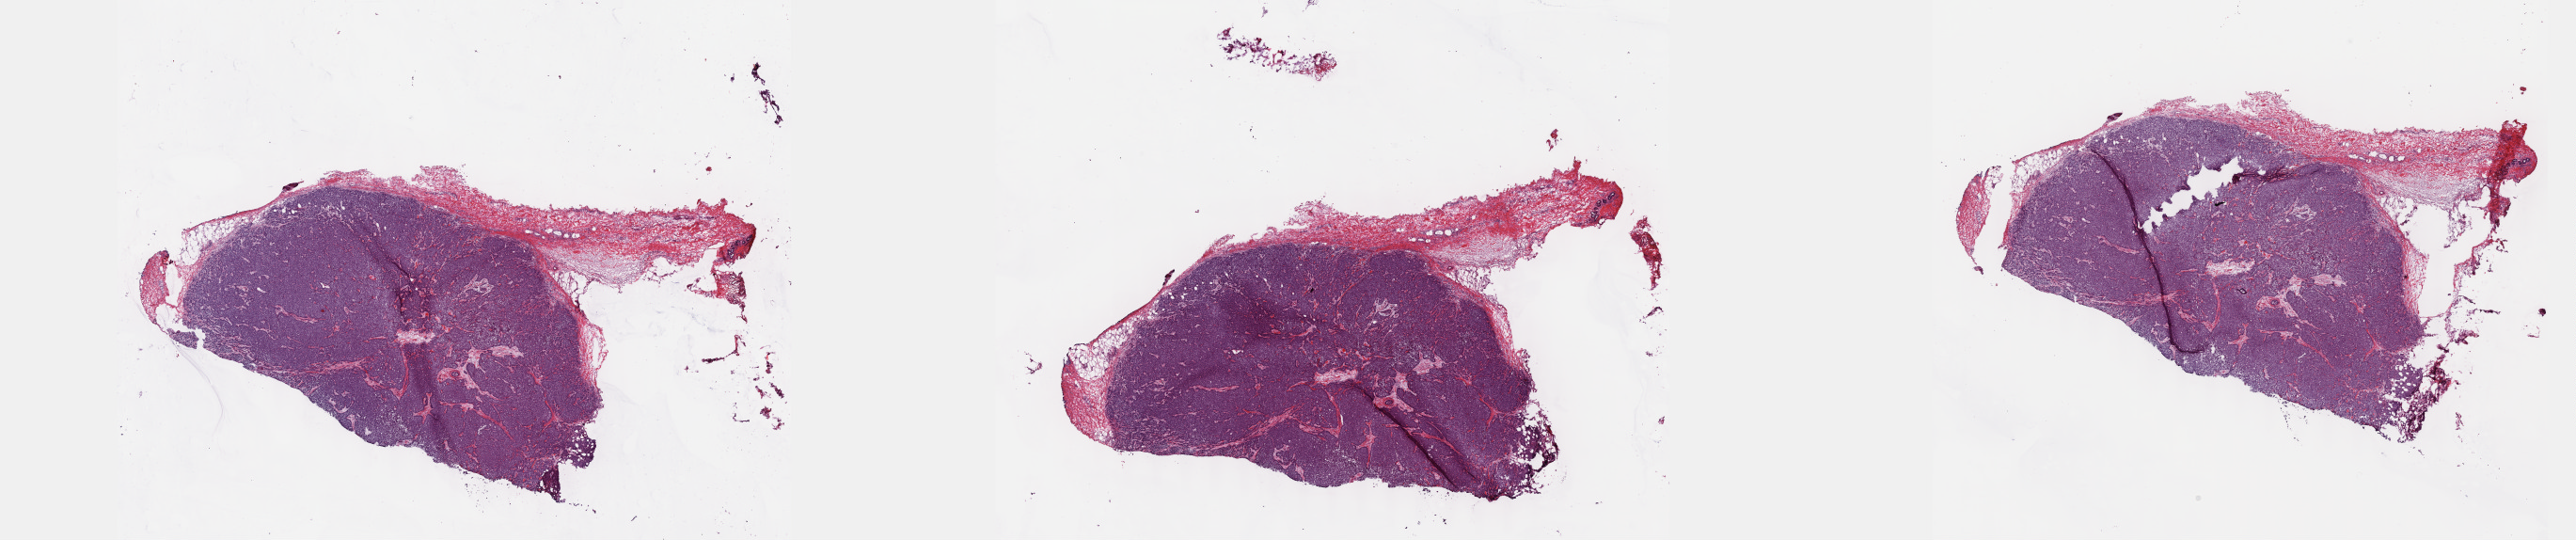
H&E whole-slide image — whole scanned area (about 44.3 x 9.3 mm) shown as a low-resolution overview, frozen section, sample: primary tumour, breast. Patient: female, age at initial diagnosis 51 years. Pathologist review of this section (percent, as recorded): tumour cells 90%, tumour nuclei 90%, normal cells 4%, stromal cells 4%, necrosis 2%. Inflammatory infiltration, as recorded: lymphocyte infiltration 2%, monocyte infiltration 1%, neutrophil infiltration 1%.
* histologic diagnosis: Infiltrating duct carcinoma, NOS
* lymph nodes positive (case pathology): 3 of 15 examined
* TNM: T1c N1a MX
* AJCC pathologic stage: IIA (7th edition)
* laterality: right